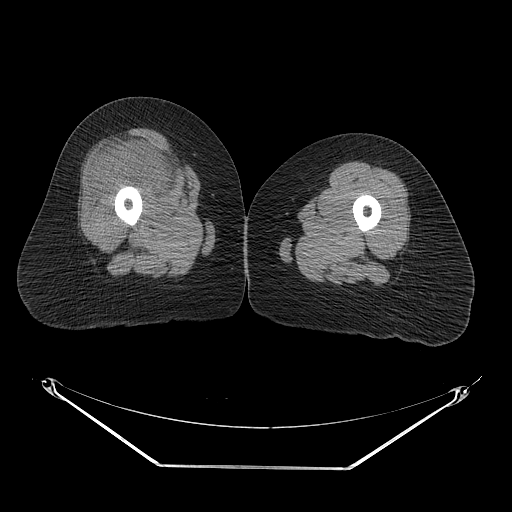
CT of an extremity soft-tissue mass (from a PET/CT study), one axial slice; position 26 of 267 along the scan axis; reconstruction kernel STANDARD; 140 kVp; soft-tissue window (W 400 / L 40 HU); 3.75 mm slice thickness; 512 × 512 image matrix, field of view 500 × 500 mm. Female patient. Case-level facts recorded for this patient, not image findings: histological type: malignant solitary fibrous tumor; grade: intermediate; site of the primary tumour: right thigh.
Annotated regions visible in this slice (expert contour drawn on MRI and transferred to this co-registered scan by the dataset authors):
- gross tumour volume including surrounding oedema: box from (x=103, y=130) to (x=200, y=206) px
- gross tumour volume (mass): (x=105, y=137)–(x=186, y=199)